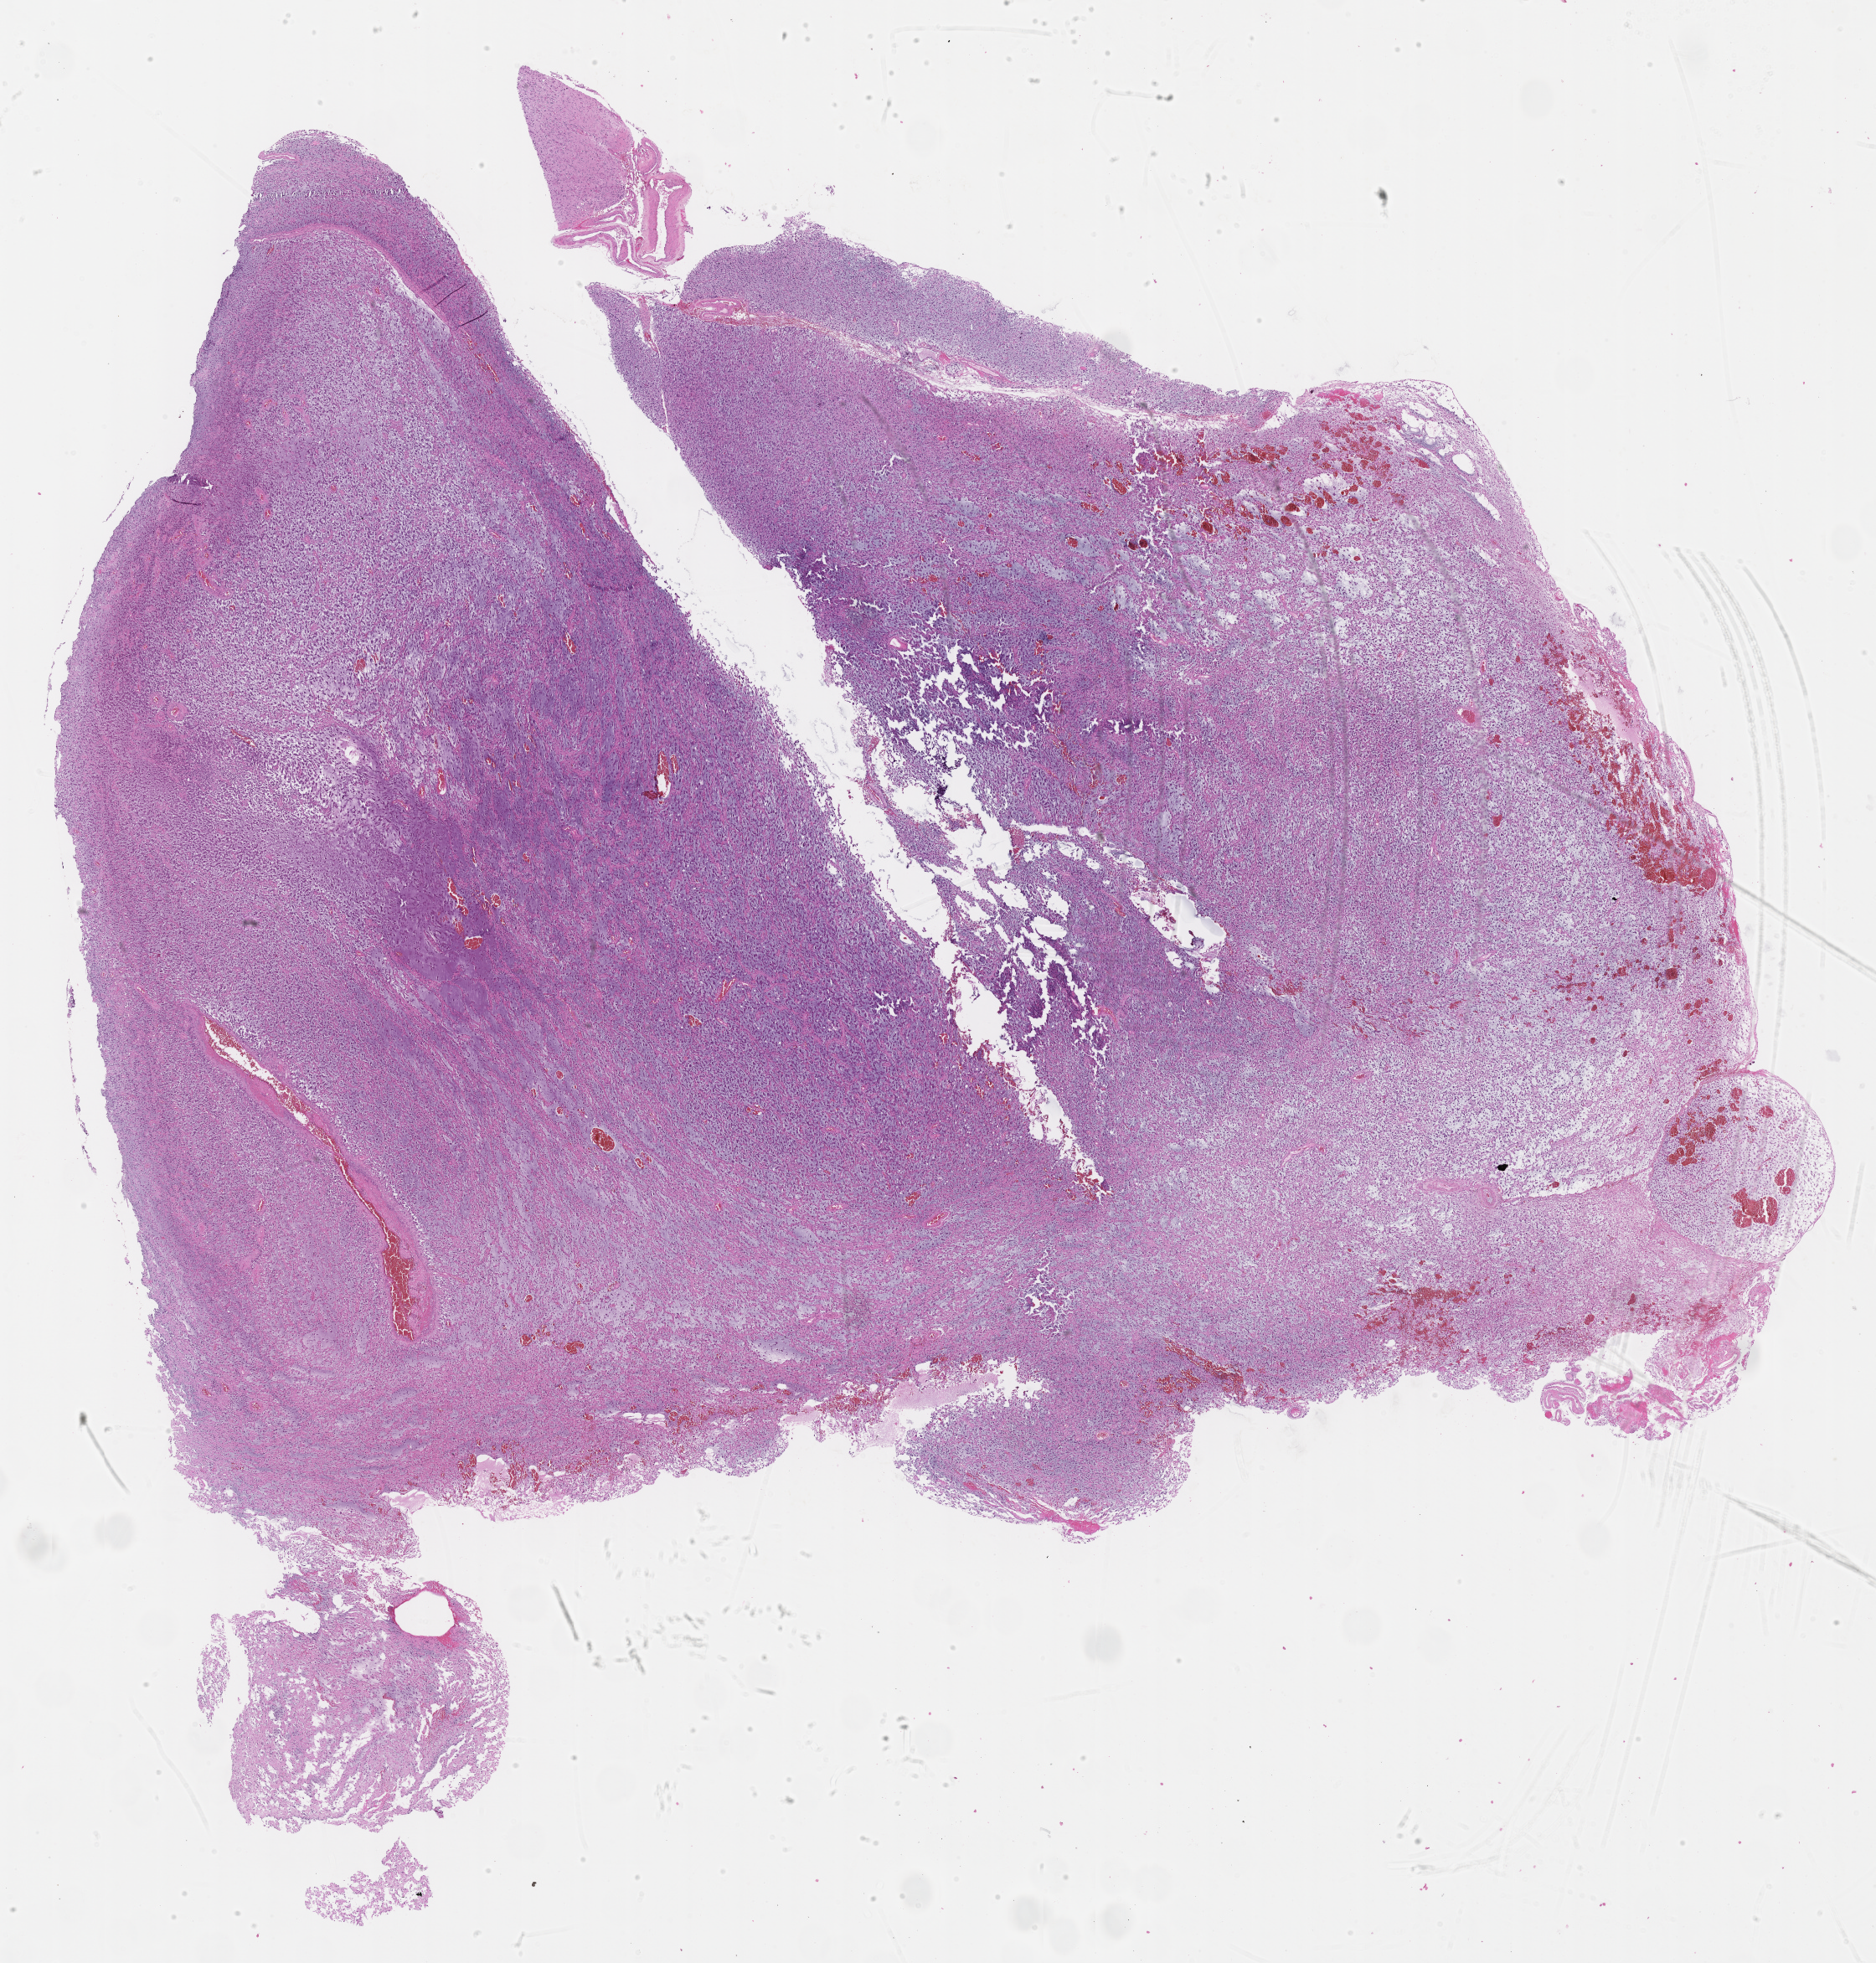
Whole-slide histology image, H&E — whole scanned area (about 18.2 x 19.0 mm, acquisition: 40x scan) shown as a low-resolution overview, formalin-fixed paraffin-embedded (FFPE) diagnostic section, primary tumour sample from the brain. Patient: female, age at initial diagnosis 31 years.
Diagnosis: Glioblastoma.